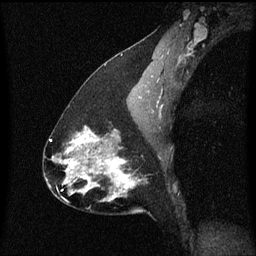
Breast MRI (dynamic contrast-enhanced), one sagittal slice. Slice 35 of 60 in the series (ordered by position). Dynamic contrast-enhanced series, image 2 of 3 at this slice position (ordered by acquisition). 1.5 T. TE 4.2 ms, TR 8.4 ms. 2 mm slice thickness. 256 × 256 image matrix, field of view 200 × 200 mm. Female patient, age 47 years.
Outlined on this slice (semi-automatically segmented with operator editing):
- analysis volume of interest (the breast-tissue region the enhancement analysis was run in; not a lesion): bounding box (x1, y1, x2, y2) in pixels: (81, 138, 145, 213)
- tumour enhancement mask (voxels above the 70 % enhancement threshold inside the analysis volume of interest): (81, 138, 135, 195)